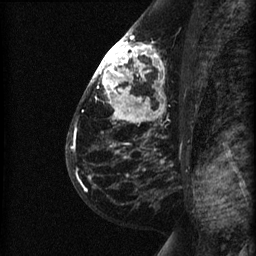
Breast MRI (dynamic contrast-enhanced), one sagittal slice; position 38 of 60 along the scan axis; dynamic contrast-enhanced series, image 2 of 3 at this slice position (ordered by acquisition); 1.5 T; TE 4.2 ms, TR 22.7 ms; 1.5 mm slice thickness; 256 × 256 image matrix. Patient: female, 48 years. From the clinical record (not read from this slice): setting: breast cancer imaged before/during neoadjuvant chemotherapy; receptor status: triple-negative.
Annotated regions visible in this slice (semi-automatic segmentation, software-assisted and operator-edited):
- analysis volume of interest (the breast-tissue region the enhancement analysis was run in; not a lesion): bounding box <89,27,191,180> (left, top, right, bottom; pixels)
- tumour enhancement mask (voxels above the 90 % enhancement threshold inside the analysis volume of interest): <92,32,162,109>